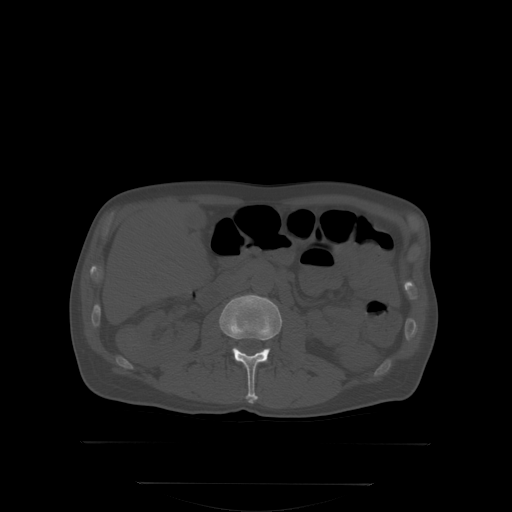
CT including the spine, one axial slice; slice 135 of 350 in the series (ordered by position); bone window (W 1800 / L 400 HU); 512 × 512 image matrix, field of view 500 × 500 mm. Patient: male, 58 years. From the clinical record (not read from this slice): primary cancer: prostate.
Outlined on this slice (semi-automatic segmentation, software-assisted and operator-edited):
- L2 vertebra: bounding box (x1, y1, x2, y2) in pixels: (221, 296, 281, 401)